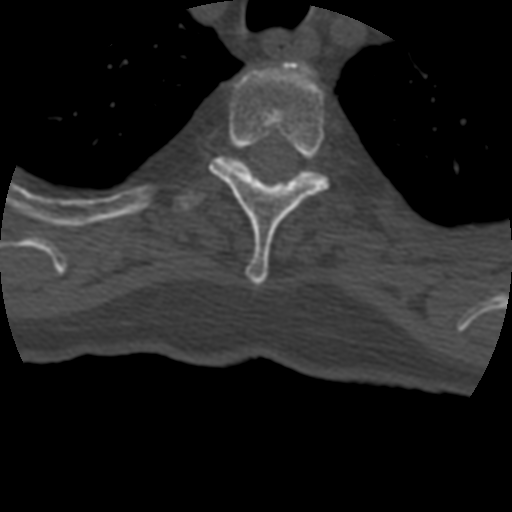
CT including the spine, one axial slice; position 351 of 399 along the scan axis; 120 kVp; bone window (W 1800 / L 400 HU); 1.25 mm slice thickness; 512 × 512 image matrix, field of view 160 × 160 mm. Patient age 69 years. From the clinical record (not read from this slice): primary cancer: prostate.
Outlined on this slice (semi-automatically segmented with operator editing):
- T3 vertebra: bounding box (x1, y1, x2, y2) in pixels: (209, 61, 330, 285)
- T4 vertebra: (173, 157, 317, 212)